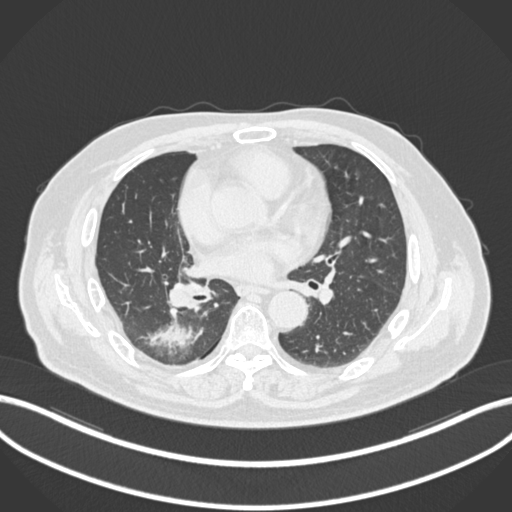
Chest CT, one axial slice; slice 91 of 218 in the series (ordered by position); lung window (W 1500 / L -600 HU); 1 mm slice thickness; 512 × 512 image matrix, field of view 400 × 400 mm. Male patient, age 68 years. Case-level facts recorded for this patient, not image findings: clinical TNM (as recorded): T2a N0 M0.
Outlined on this slice (rectangle marked by the reading radiologist):
- lung tumour (recorded histology: adenocarcinoma): bounding box <144,317,202,351> (left, top, right, bottom; pixels)